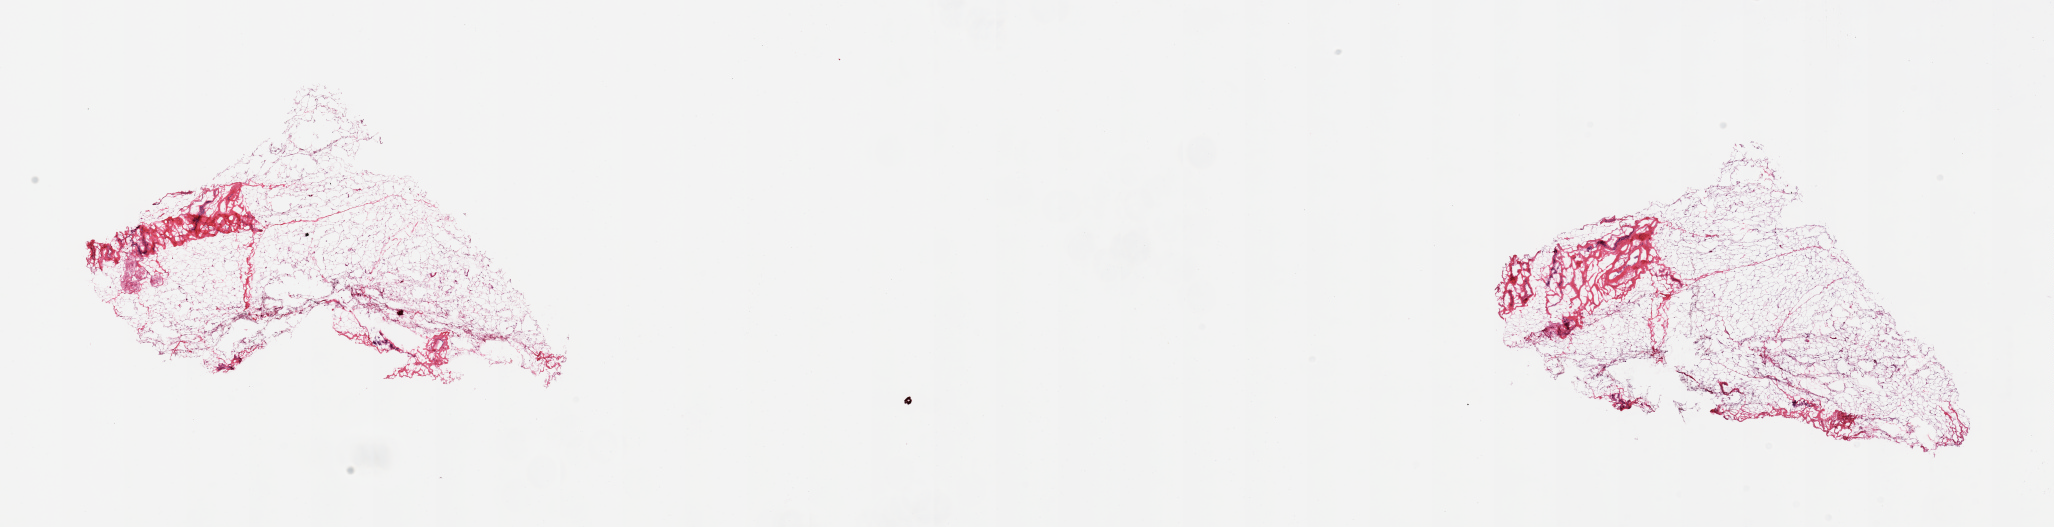
Haematoxylin and eosin whole-slide image — a low-resolution overview of the entire scanned area, about 32.5 x 8.3 mm (slide scanned at 20x). Donor sex: female.
• specimen: frozen section (dry ice); sampled site (target tissue): breast; tissue donor sample